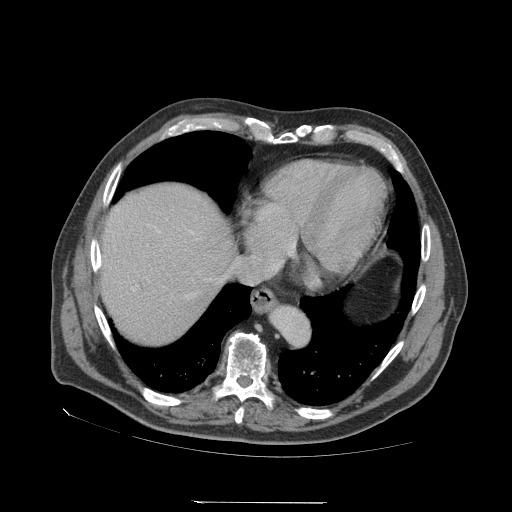
Contrast-enhanced abdominal CT (liver protocol), one axial slice; position 64 of 83 along the scan axis; 140 kVp; soft-tissue window (W 400 / L 40 HU); 2.5 mm slice thickness; 512 × 512 image matrix, field of view 460 × 460 mm. From the clinical record (not read from this slice): diagnosis: hepatocellular carcinoma (patient treated with transarterial chemoembolisation; whether this scan precedes or follows treatment is not stated here); TNM stage (as recorded): Stage-I; Child-Pugh class: A; tumour differentiation: well differentiated; tumour nodularity: uninodular.
Outlined on this slice (semi-automatically segmented with operator editing):
- abdominal aorta: bounding box [x1, y1, x2, y2] px = [272, 308, 308, 344]
- liver parenchyma outside the tumour (the mass and vessels are separate outlines, so this box may not span the whole liver): [100, 184, 232, 342]
- liver vessels: [117, 209, 194, 234]